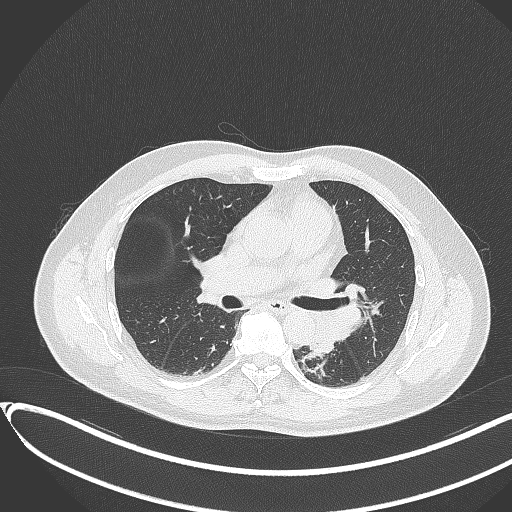
Chest CT, one axial slice; slice 193 of 417 in the series (ordered by position); reconstruction kernel B70f; lung window (W 1500 / L -600 HU); 1 mm slice thickness; 512 × 512 image matrix, field of view 400 × 400 mm. Patient: male, 54 years. Case-level facts recorded for this patient, not image findings: clinical TNM (as recorded): T3 N0 M0.
Structures marked on this image (rectangle marked by the reading radiologist):
- lung tumour (recorded histology: squamous cell carcinoma): box from (x=312, y=321) to (x=339, y=360) px